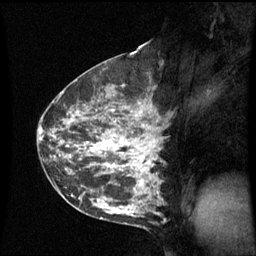
Breast MRI (dynamic contrast-enhanced), one sagittal slice. Position 32 of 60 along the scan axis. Dynamic contrast-enhanced series, image 2 of 3 at this slice position (ordered by acquisition). 1.5 T. TE 4.2 ms, TR 8.9 ms. 2.4 mm slice thickness. 256 × 256 image matrix, field of view 210 × 210 mm. Patient: female, 42 years. From the clinical record (not read from this slice): setting: breast cancer imaged before/during neoadjuvant chemotherapy; receptor status: HER2-positive.
Structures marked on this image (semi-automatic segmentation, software-assisted and operator-edited):
- analysis volume of interest (the breast-tissue region the enhancement analysis was run in; not a lesion): box from (x=62, y=93) to (x=165, y=210) px
- tumour enhancement mask (voxels above the 70 % enhancement threshold inside the analysis volume of interest): (x=85, y=103)–(x=158, y=186)